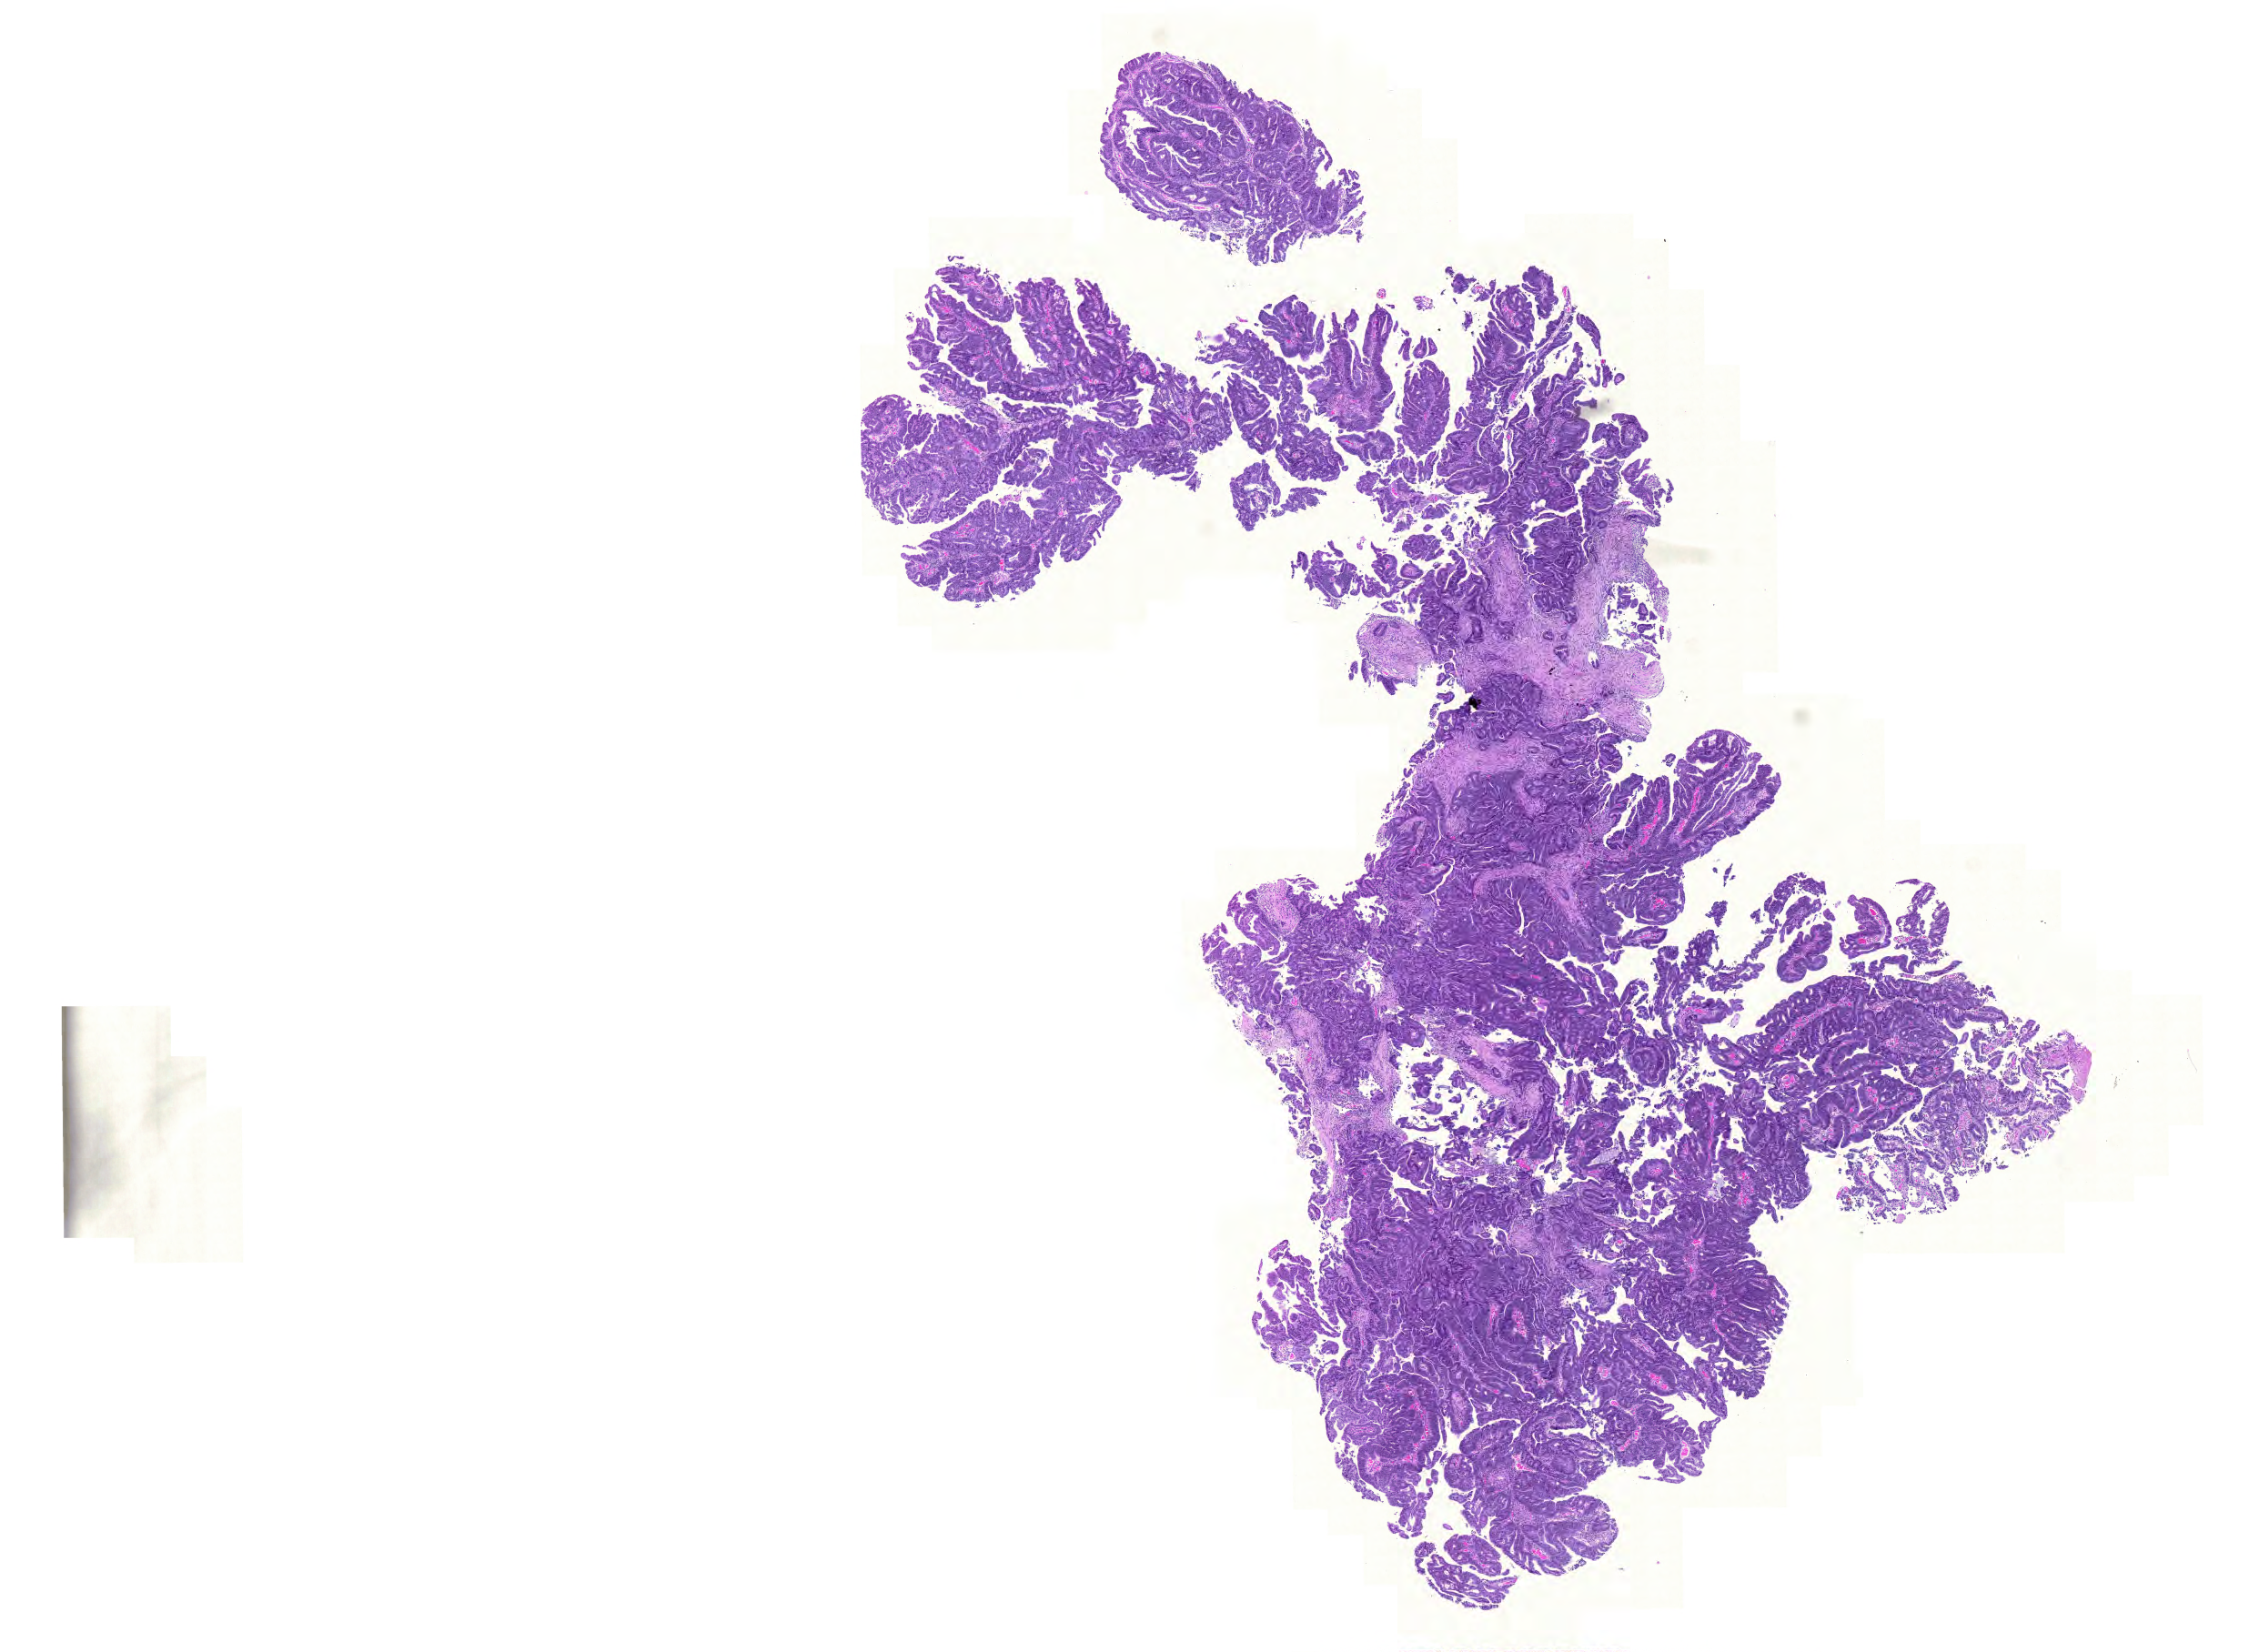
Digitized Hematoxylin and eosin (H&E) stained tissue section (whole slide) — low-resolution overview of the scanned area, about 18.4 x 13.5 mm, formalin-fixed paraffin-embedded (FFPE) diagnostic section, sample: primary tumour, rectum. Female, age 85 years at initial diagnosis.
* lymph nodes positive (case pathology): 3 of 13 examined
* AJCC pathologic stage: IV (6th edition)
* pathologic diagnosis: Adenocarcinoma, NOS
* TNM: T3 N1 M1